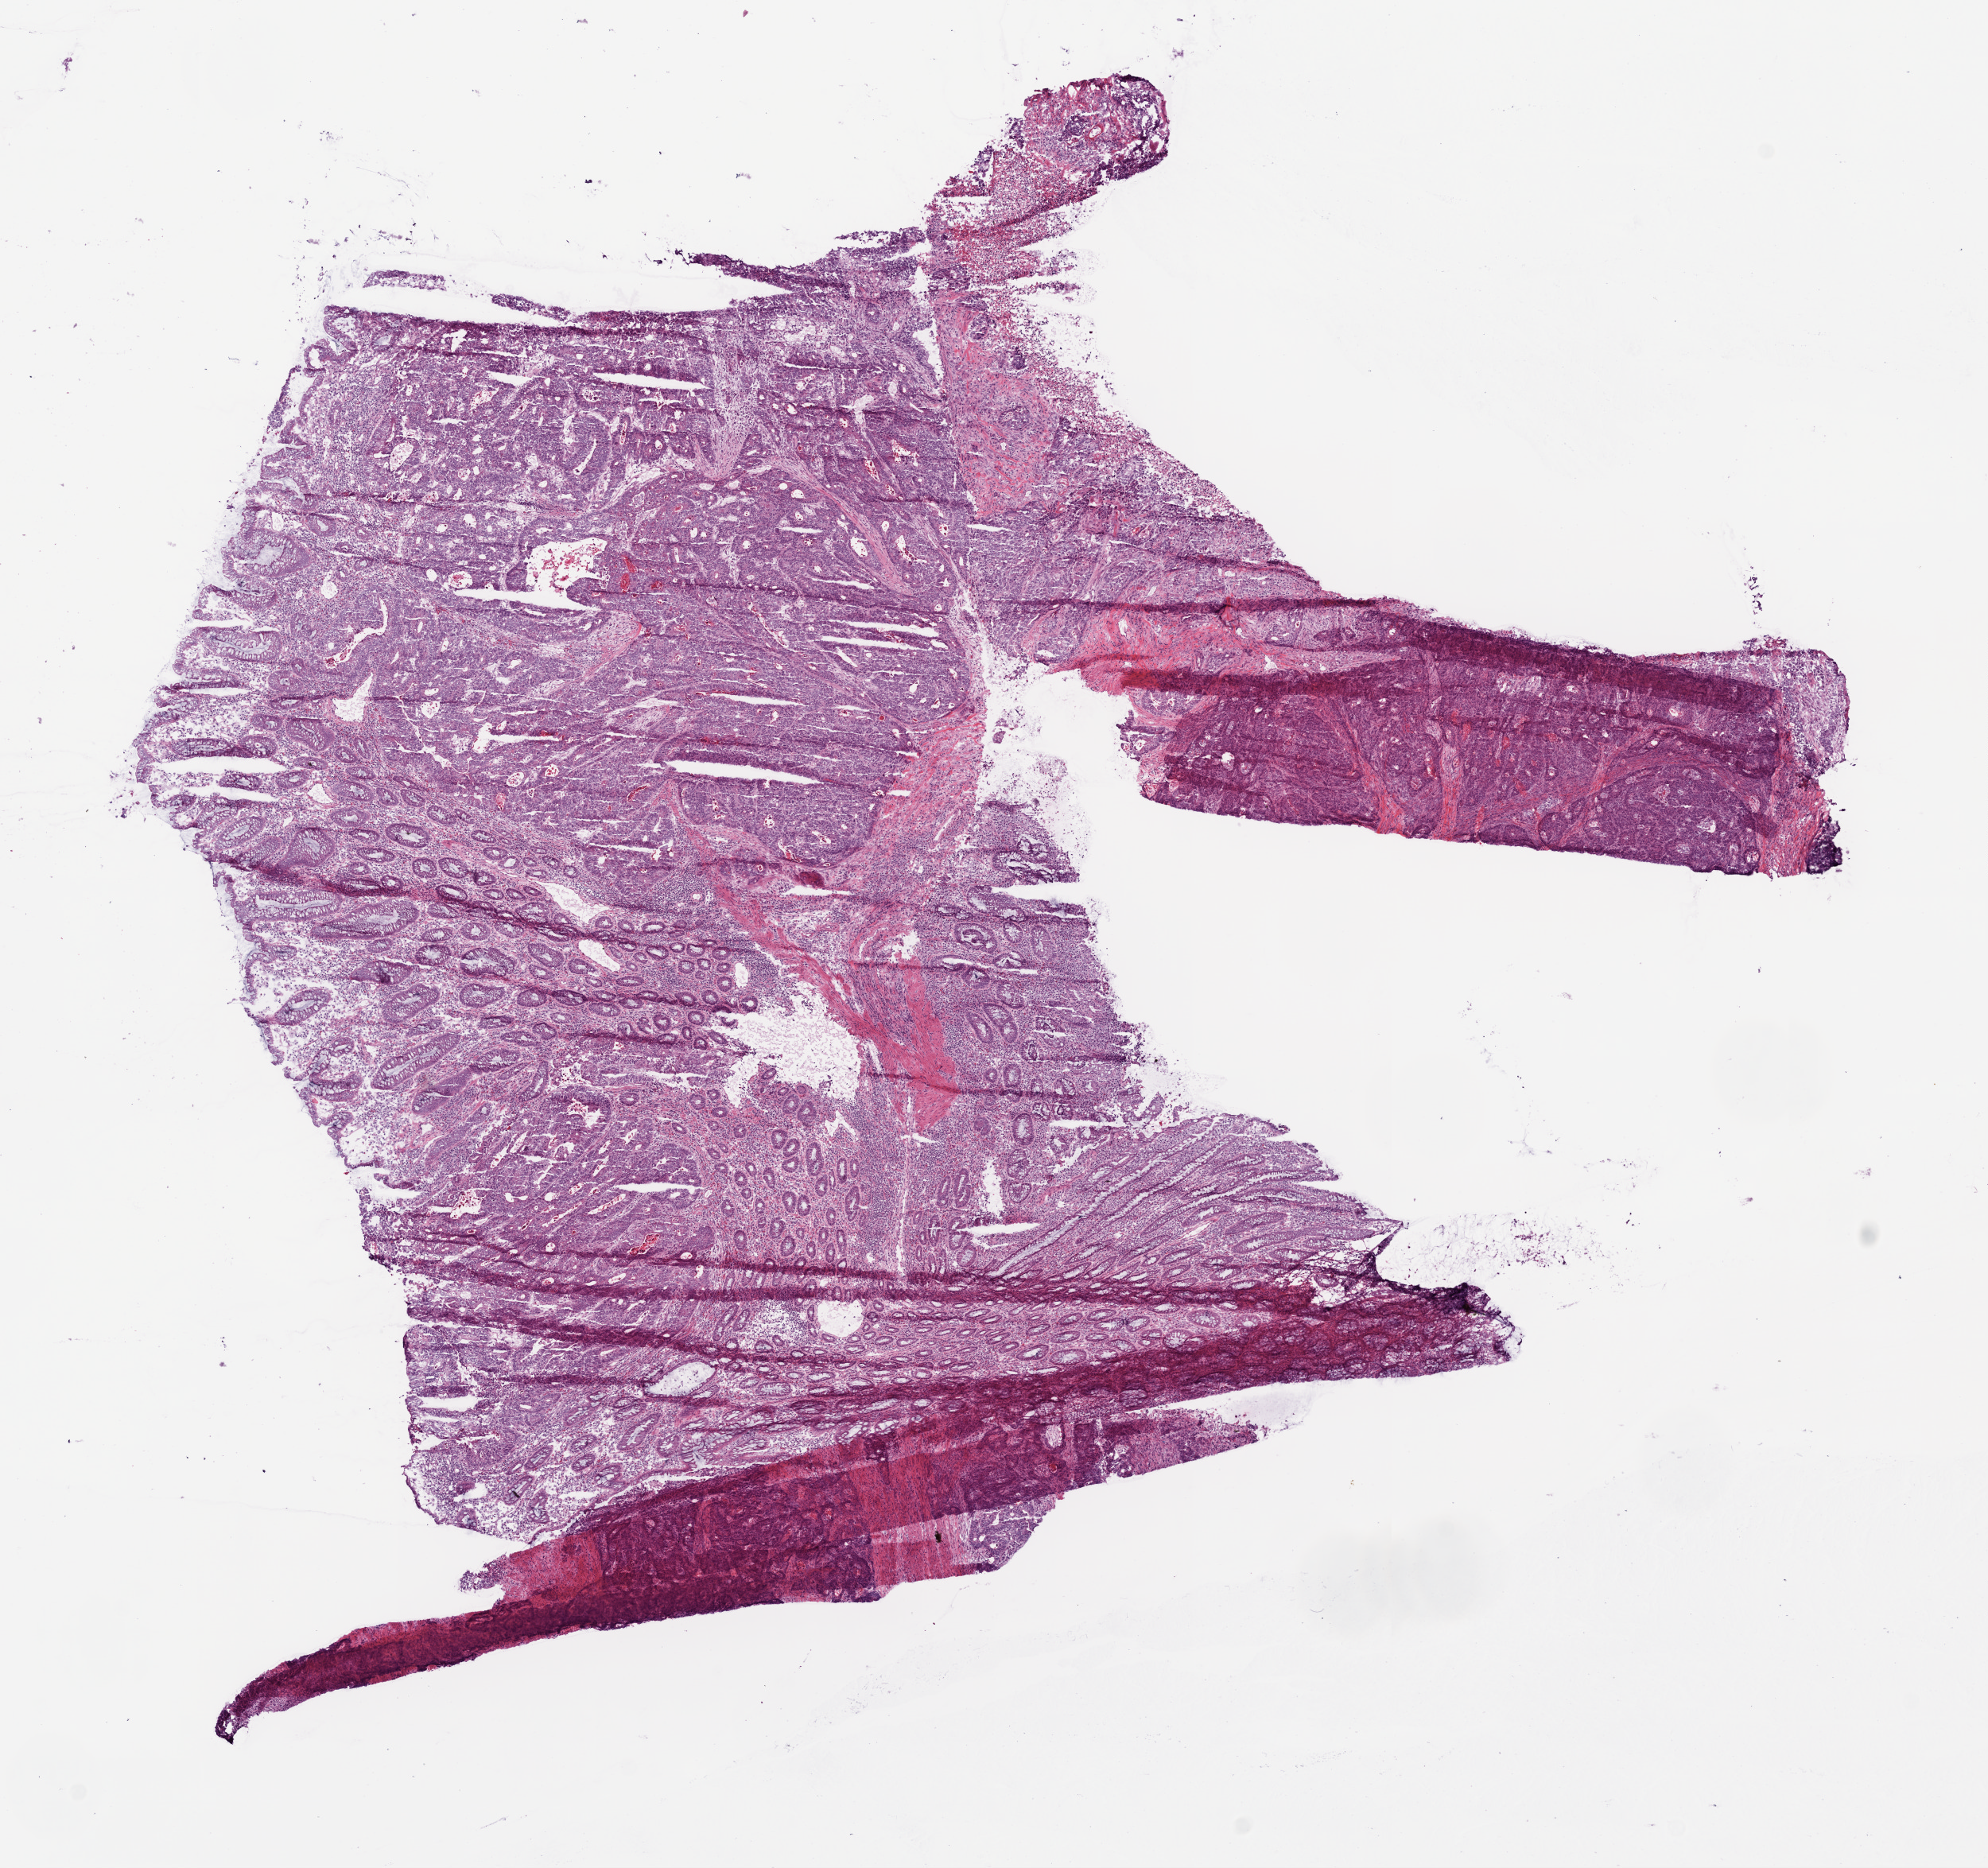
Digitized H&E-stained tissue section (whole slide) — whole scanned area (about 10.0 x 9.4 mm, acquisition: 20x scan) shown as a low-resolution overview; frozen section; primary tumour sample from the rectum. Male, age 77 years at initial diagnosis. Pathologist review of this section (percent, as recorded): tumour cells 50%, tumour nuclei 60%, normal cells 40%, stromal cells 5%, necrosis 5%.
AJCC pathologic stage: IVA (7th edition). Histologic diagnosis: Adenocarcinoma, NOS. Lymph nodes positive (case pathology): 21 of 34 examined.